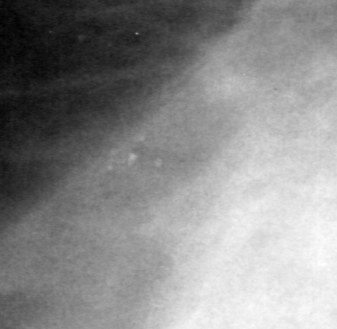
Cropped region of a digitized screen-film mammogram centred on a radiologist-marked abnormality, left breast, MLO view.
- Finding: calcifications, morphology pleomorphic, distribution clustered; BI-RADS assessment category 4; pathology (as recorded): benign.